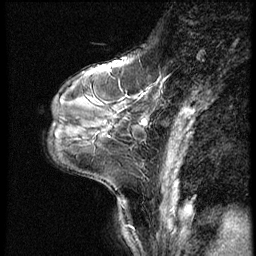
Breast MRI (dynamic contrast-enhanced), one sagittal slice; slice 23 of 62 in the series (ordered by position); dynamic contrast-enhanced series, image 2 of 4 at this slice position (ordered by acquisition); 1.5 T; TE 4.2 ms, TR 9 ms; 2.5 mm slice thickness; 256 × 256 image matrix, field of view 180 × 180 mm. Patient: female, 46 years. From the clinical record (not read from this slice): setting: breast cancer imaged before/during neoadjuvant chemotherapy; receptor status: HER2-positive.
Outlined on this slice (semi-automatic segmentation, software-assisted and operator-edited):
- analysis volume of interest (the breast-tissue region the enhancement analysis was run in; not a lesion): bounding box [x1, y1, x2, y2] px = [84, 80, 176, 140]
- tumour enhancement mask (voxels above the 140 % enhancement threshold inside the analysis volume of interest): [142, 120, 147, 125]